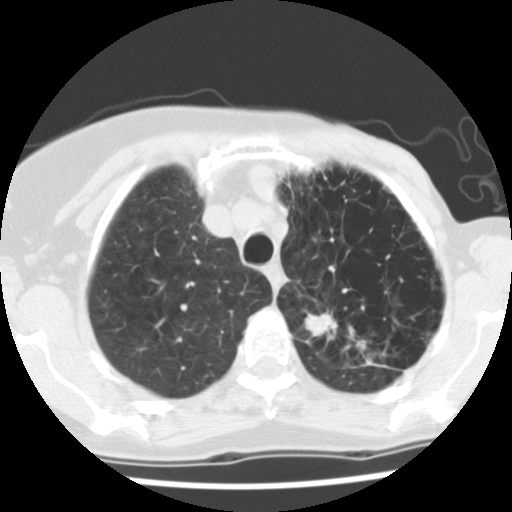
Low-dose screening chest CT, one axial slice. Position 103 of 128 along the scan axis. Reconstruction kernel STANDARD. Lung window (W 1500 / L -600 HU). 2.5 mm slice thickness. 512 × 512 image matrix, field of view 290 × 290 mm.
Annotated regions visible in this slice (expert manual segmentation):
- lesion 1 (tumor, upper lobe of left lung): box from (x=305, y=312) to (x=337, y=341) px